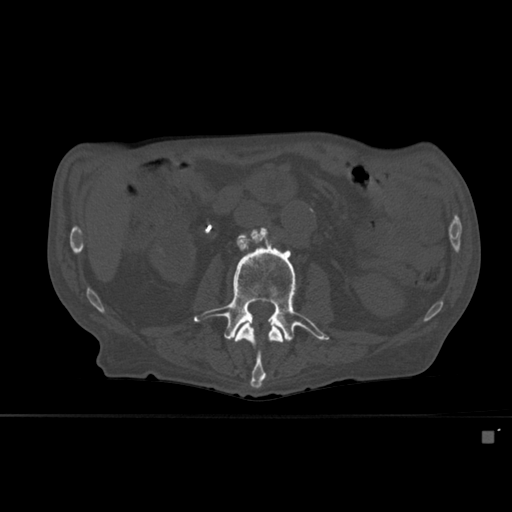
CT including the spine, one axial slice. Slice 219 of 527 in the series (ordered by position). Bone window (W 1800 / L 400 HU). 1.5 mm slice thickness. 512 × 512 image matrix. Patient: male, 78 years. From the clinical record (not read from this slice): primary cancer: prostate.
Outlined on this slice (semi-automatic segmentation, software-assisted and operator-edited):
- L2 vertebra: bounding box [x1, y1, x2, y2] px = [233, 323, 284, 389]
- L3 vertebra: [194, 228, 329, 342]
- L4 vertebra: [240, 227, 264, 238]